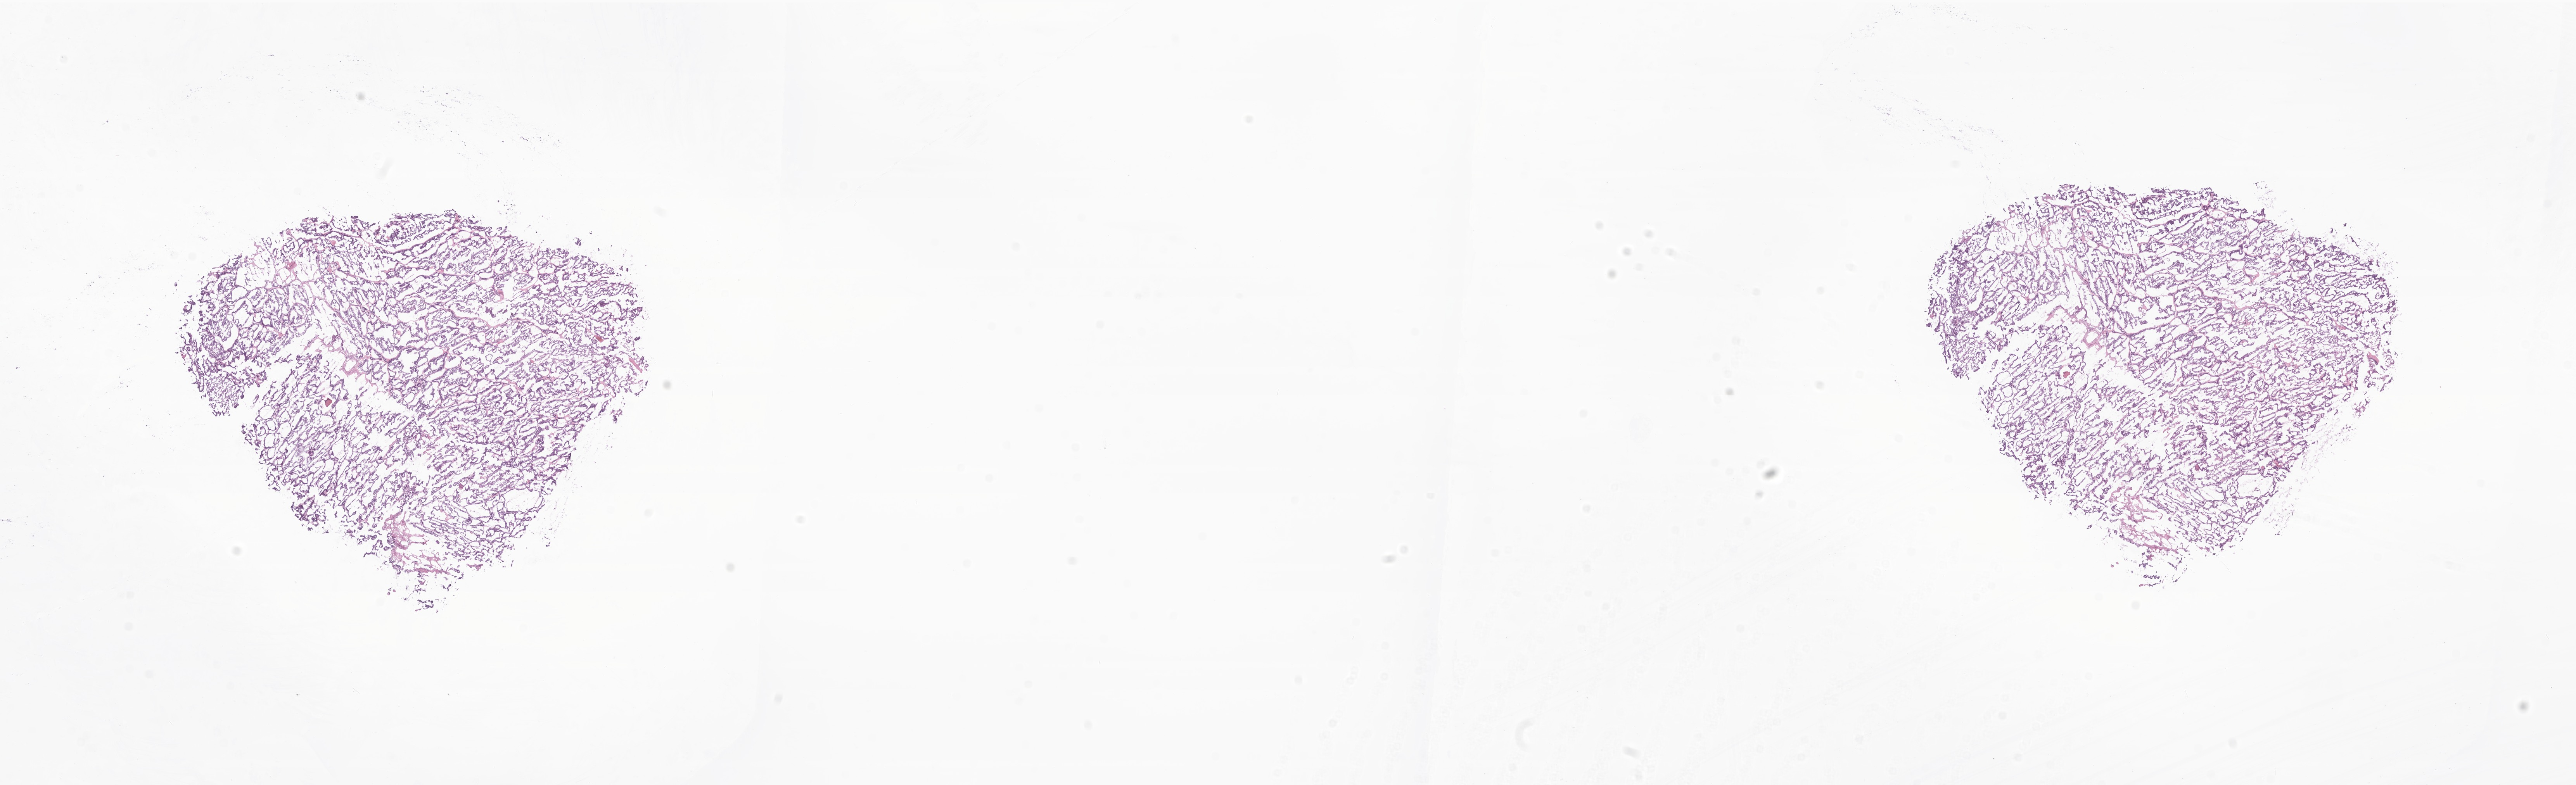
H&E whole-slide image of tumor tissue from the thyroid — low-resolution overview of the scanned area, about 28.0 x 8.5 mm, frozen section (OCT-embedded). Patient: male, age 100 months.
- diagnosis: Papillary adenocarcinoma, NOS